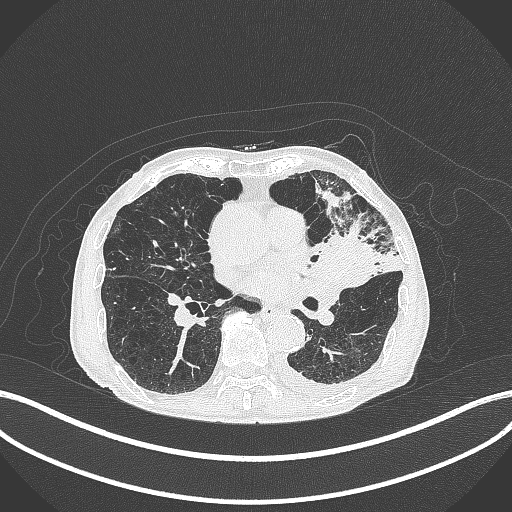
Chest CT, one axial slice. Position 184 of 385 along the scan axis. Reconstruction kernel B70f. Lung window (W 1500 / L -600 HU). 1 mm slice thickness. 512 × 512 image matrix. Patient: male, 90 years or older. Case-level facts recorded for this patient, not image findings: clinical TNM (as recorded): T2b N1 M0.
Outlined on this slice (bounding box drawn by a radiologist):
- lung tumour (recorded histology: squamous cell carcinoma): bounding box <318,228,379,291> (left, top, right, bottom; pixels)